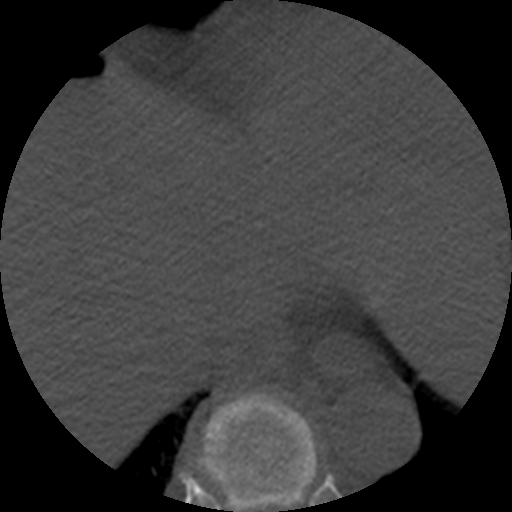
CT including the spine, one axial slice; position 298 of 508 along the scan axis; reconstruction kernel STANDARD; 120 kVp; bone window (W 1800 / L 400 HU); 512 × 512 image matrix, field of view 160 × 160 mm. Patient age 57 years. Case-level facts recorded for this patient, not image findings: primary cancer: prostate.
Annotated regions visible in this slice (semi-automatic segmentation, software-assisted and operator-edited):
- T9 vertebra: box from (x=196, y=392) to (x=318, y=512) px